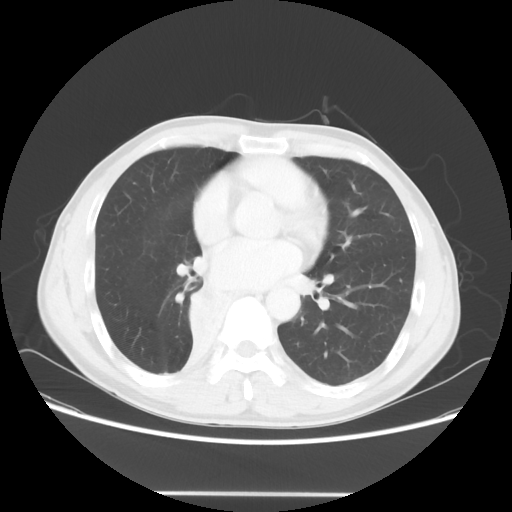
Chest CT, one axial slice. Position 29 of 62 along the scan axis. Lung window (W 1500 / L -600 HU). 5 mm slice thickness. 512 × 512 image matrix, field of view 393 × 393 mm. Patient: male, 47 years. From the clinical record (not read from this slice): clinical TNM (as recorded): T2 N0 M0; histopathological grade: G2.
Structures marked on this image (rectangle marked by the reading radiologist):
- lung tumour (recorded histology: squamous cell carcinoma): box from (x=178, y=277) to (x=225, y=336) px